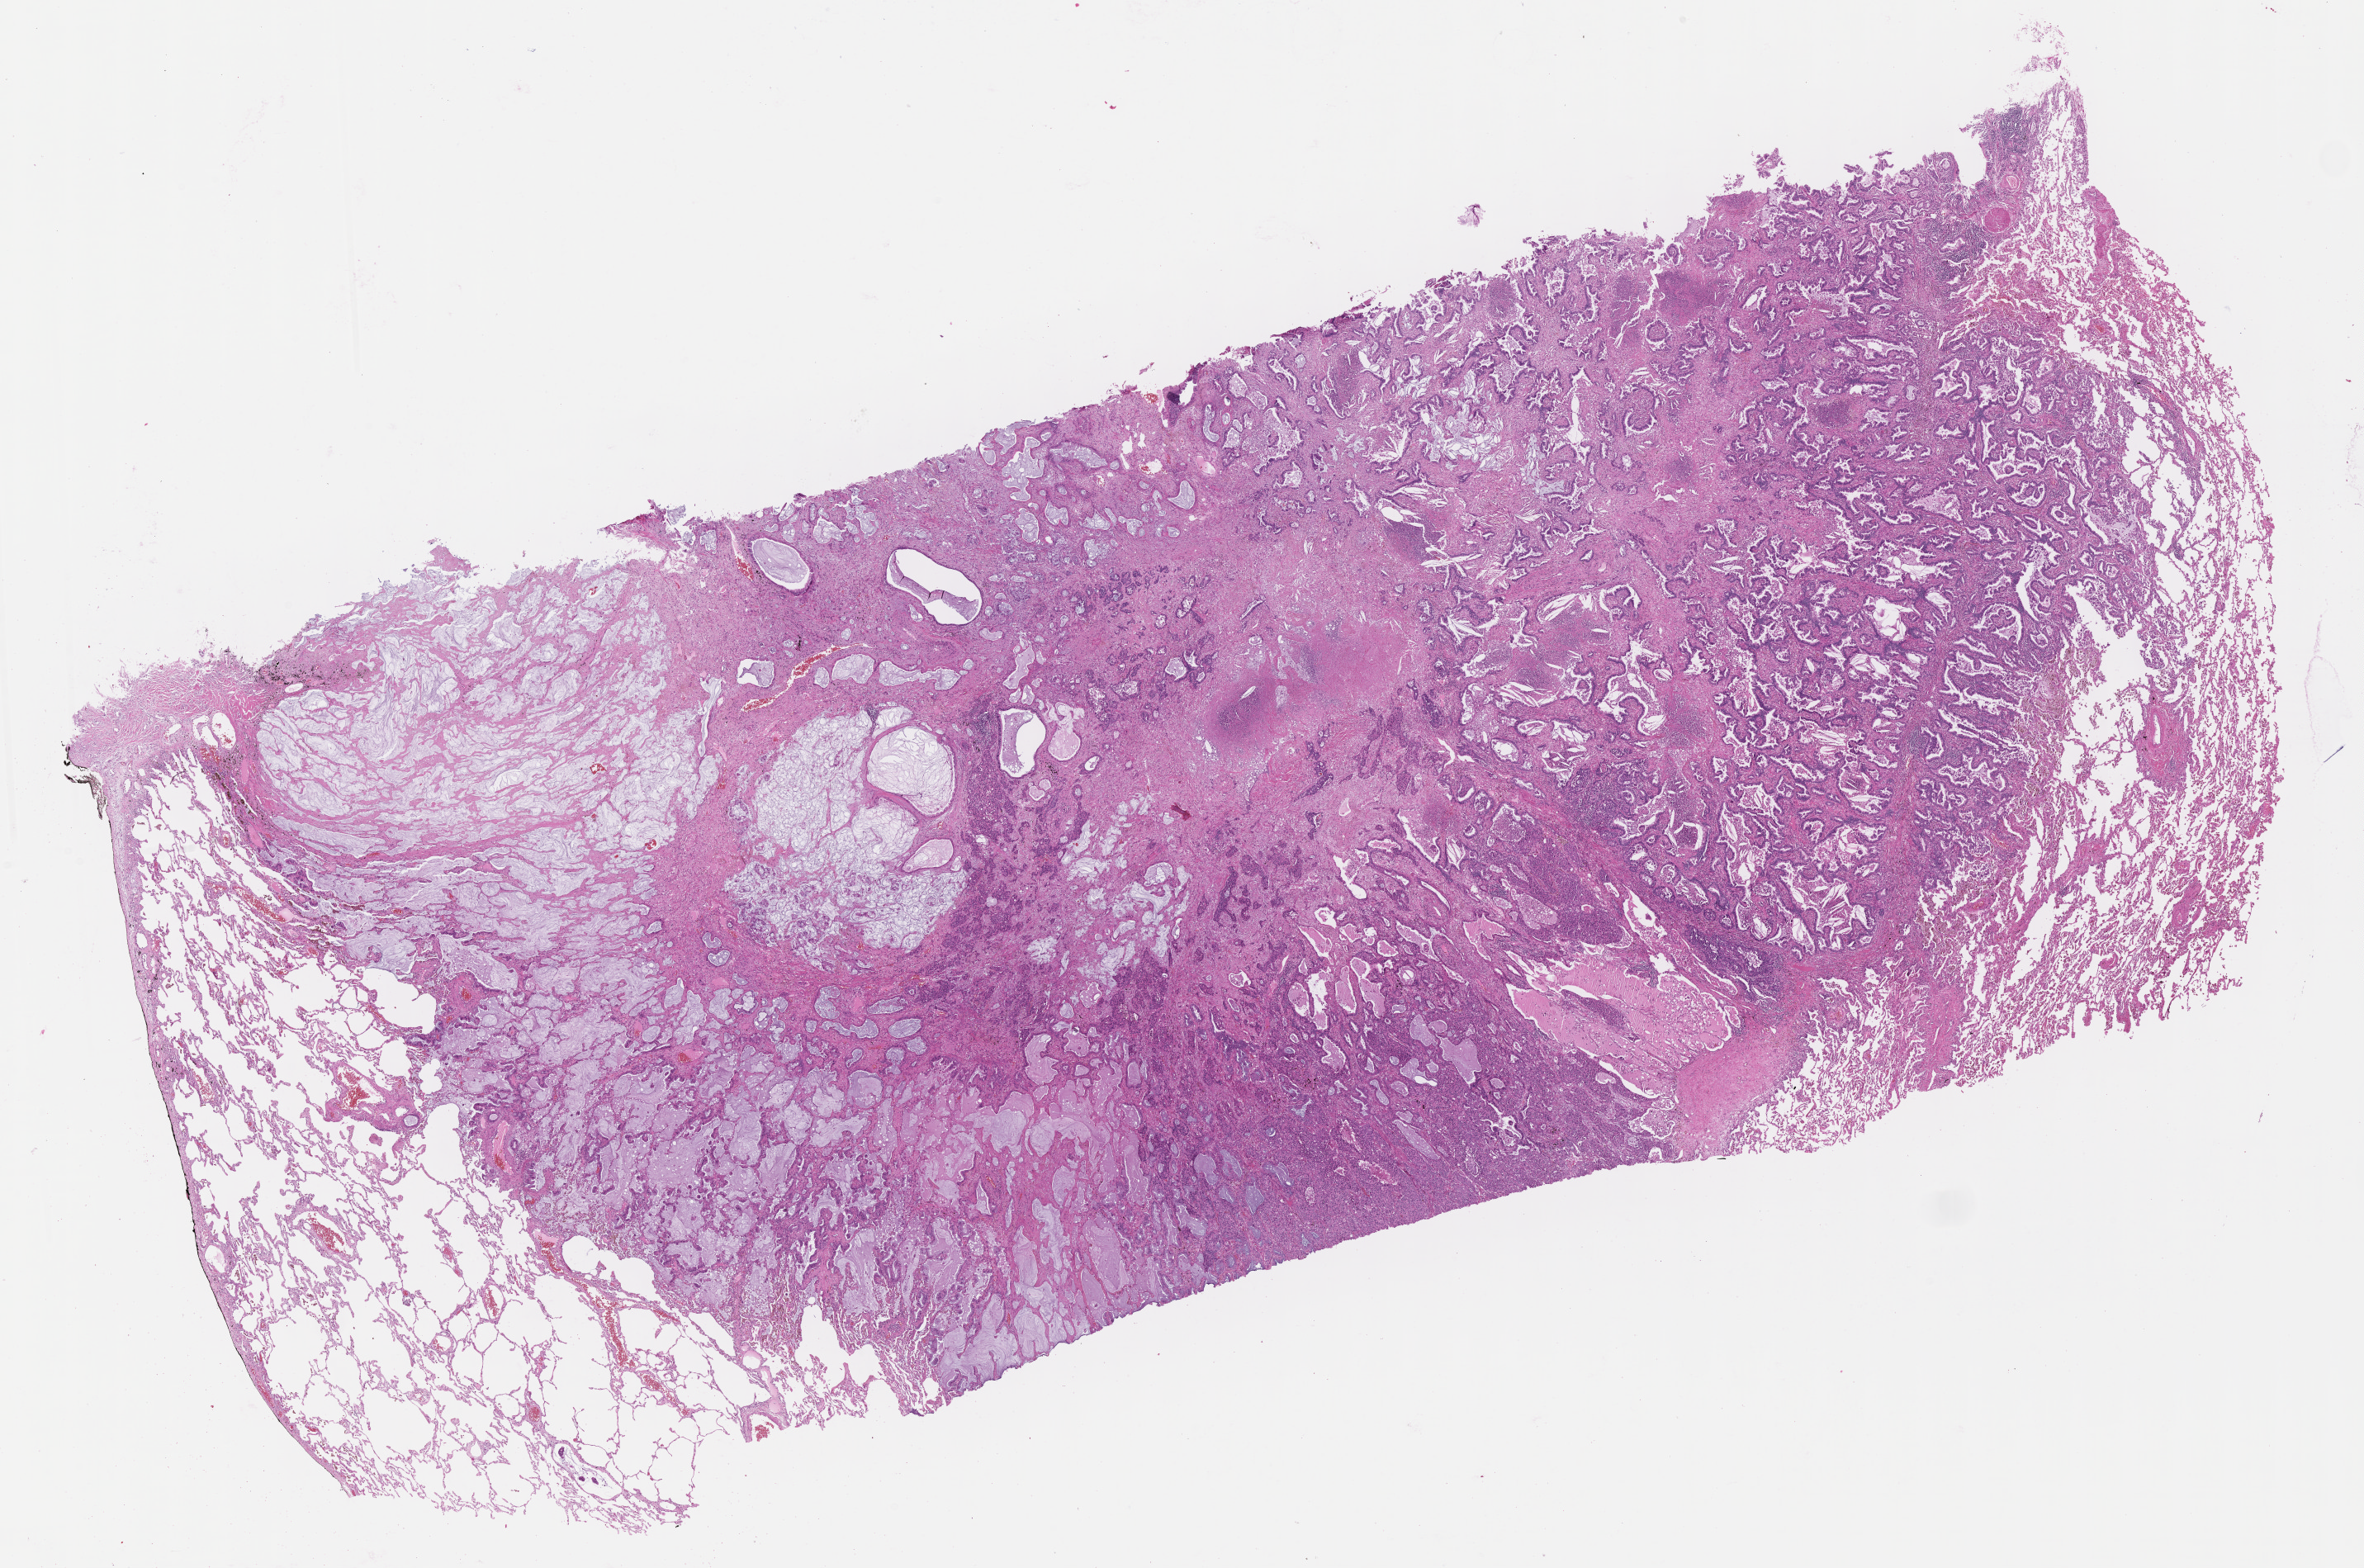
Whole-slide image, H&E stain, whole scanned area (about 23.1 x 15.4 mm) shown as a low-resolution overview, FFPE section, specimen: primary tumor, site: upper lobe of right lung. Patient male; 63 years old. Slide review estimates, as recorded: tumor cells 60%, tumor nuclei 70%, stromal cells 10%, necrosis 10%, normal cells 20%. Inflammatory infiltration, as recorded: lymphocyte infiltration 0%, monocyte infiltration 0%, neutrophil infiltration 0%.
- diagnosis: Adenocarcinoma with mixed subtypes
- section: top of the tissue portion
- AJCC pathologic stage: Stage IB